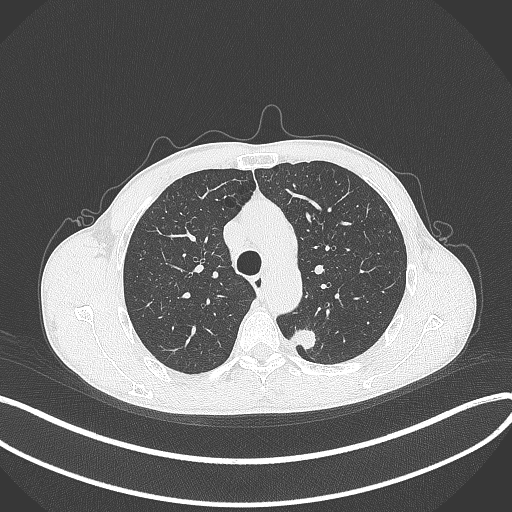
Chest CT, one axial slice; position 286 of 429 along the scan axis; reconstruction kernel B70f; 120 kVp; lung window (W 1500 / L -600 HU); 1 mm slice thickness; 512 × 512 image matrix, field of view 400 × 400 mm. Patient: male, 51 years. From the clinical record (not read from this slice): clinical TNM (as recorded): T2a N1 M1.
Annotated regions visible in this slice (bounding box drawn by a radiologist):
- lung tumour (recorded histology: adenocarcinoma): bounding box (x1, y1, x2, y2) in pixels: (290, 324, 319, 353)